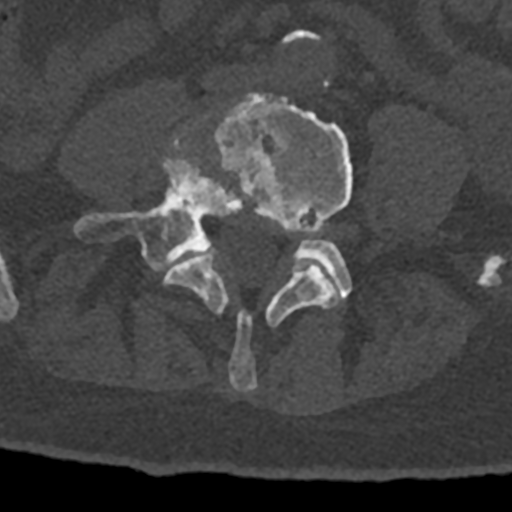
CT including the spine, one axial slice; position 232 of 797 along the scan axis; reconstruction kernel Br40s/3; bone window (W 1800 / L 400 HU); 512 × 512 image matrix, field of view 160 × 160 mm. Patient: male, 74 years. Case-level facts recorded for this patient, not image findings: primary cancer: renal; vertebrae with lytic lesions (as recorded): T10, L1, L2, L3, L4, L5.
Annotated regions visible in this slice (semi-automatic segmentation, software-assisted and operator-edited):
- L4 vertebra: bounding box <163,93,353,392> (left, top, right, bottom; pixels)
- L5 vertebra: <74,136,352,299>